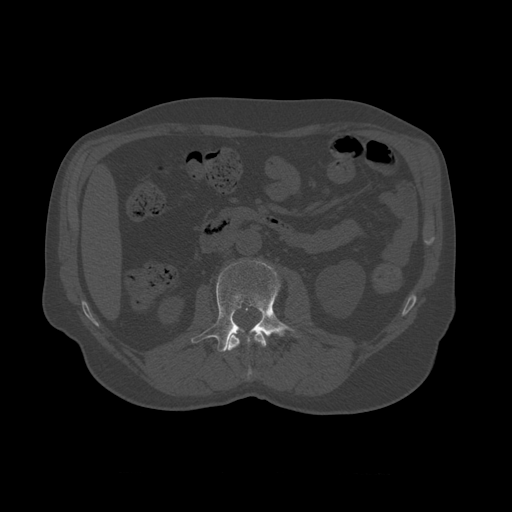
CT including the spine, one axial slice; slice 332 of 450 in the series (ordered by position); reconstruction kernel STANDARD; 120 kVp; bone window (W 1800 / L 400 HU); 1.25 mm slice thickness; 512 × 512 image matrix. Patient age 75 years. From the clinical record (not read from this slice): primary cancer: prostate.
Outlined on this slice (semi-automatically segmented with operator editing):
- L1 vertebra: bounding box <226,331,267,379> (left, top, right, bottom; pixels)
- L2 vertebra: <191,261,300,352>